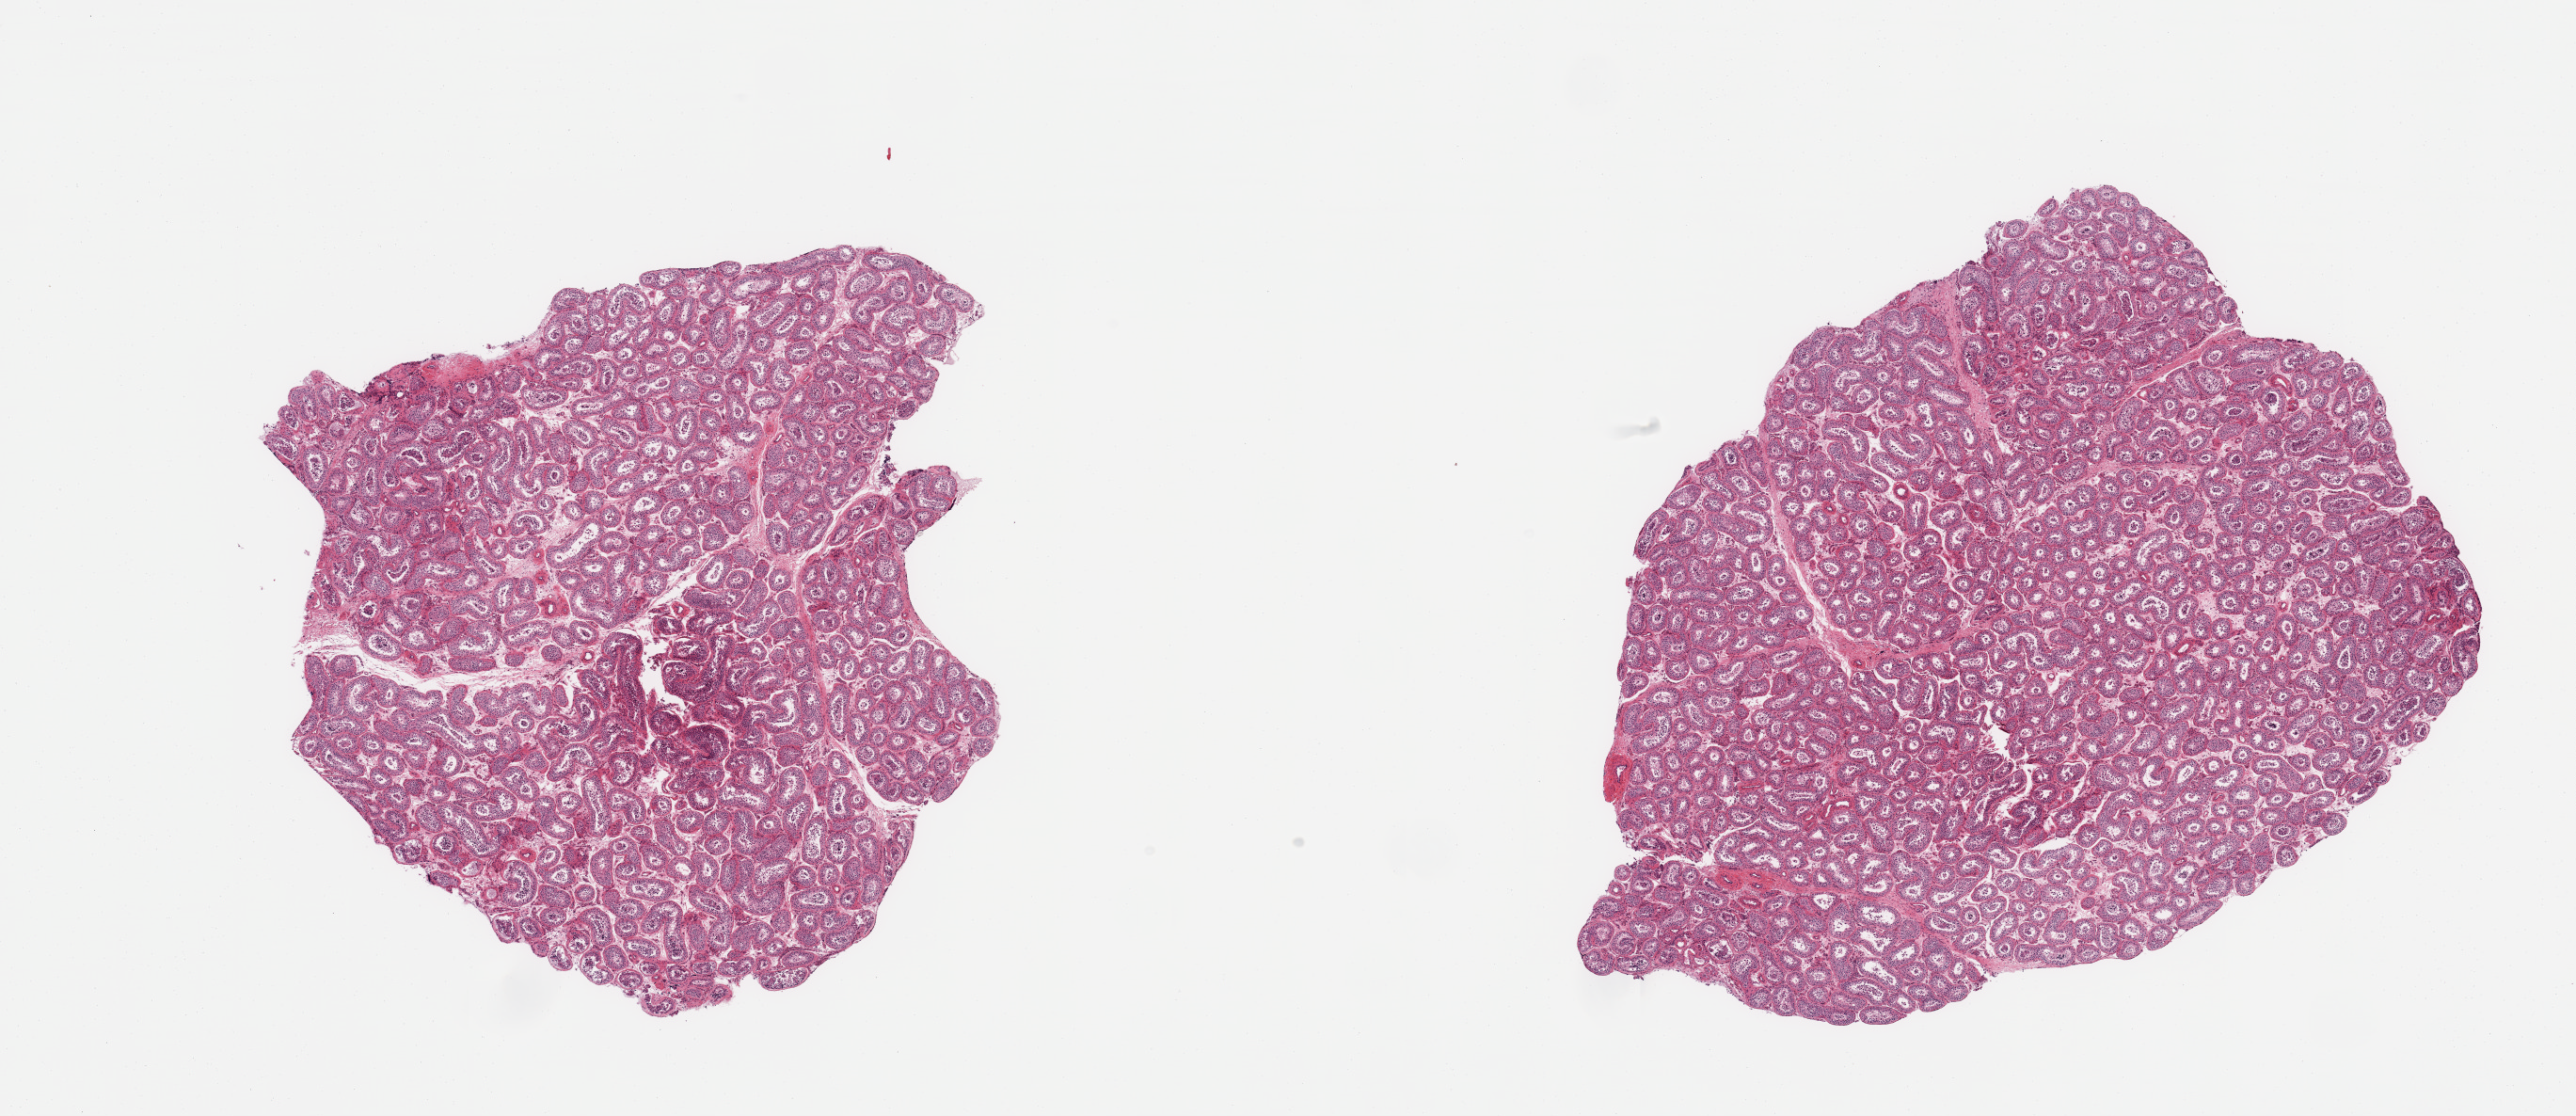
Haematoxylin and eosin whole-slide image, brightfield, whole scanned area (about 21.7 x 9.4 mm, slide scanned at 20x) shown as a low-resolution overview; PAXgene-fixed paraffin-embedded (PFPE) section; target tissue: testis; tissue donor sample.
* pathologist's review note for this sample: 2 pieces, spermatogenesis is present but appears reduced